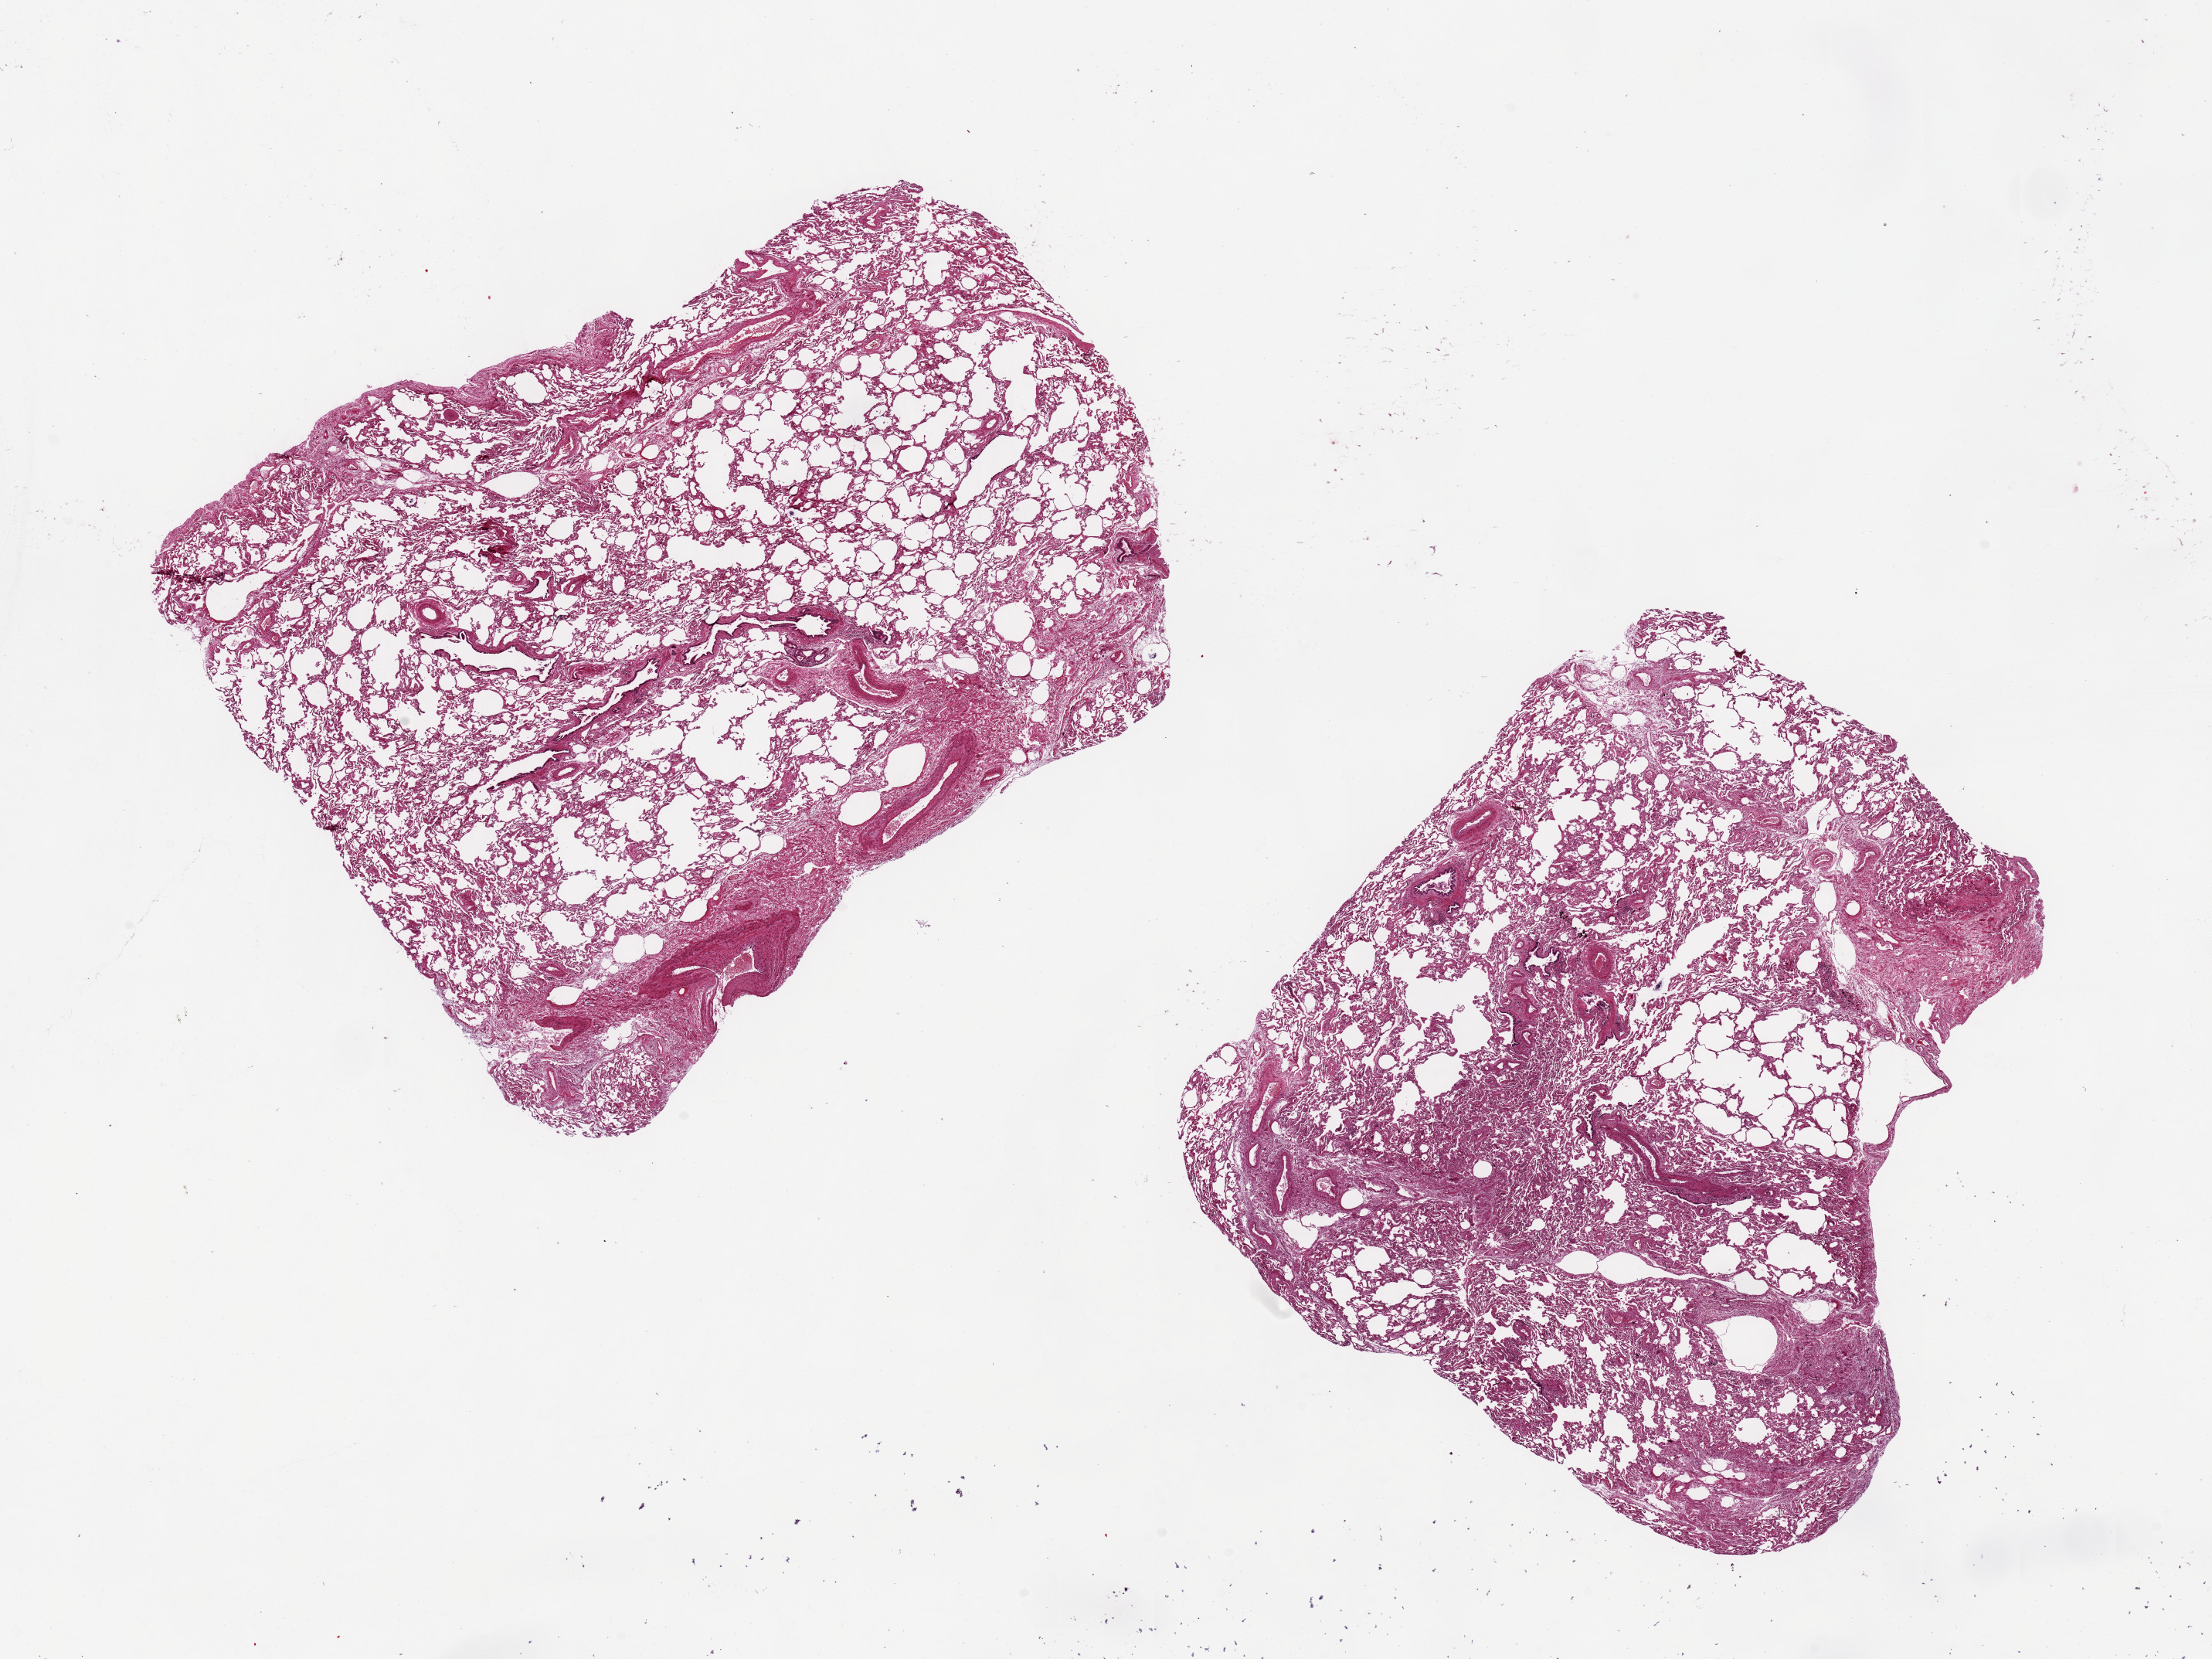
Whole-slide image, H&E stain, shown as a low-resolution overview of the whole scanned area (about 22.6 x 17.0 mm), PAXgene-fixed, paraffin-embedded tissue, sampled site (target tissue): lung, donor tissue sample. Donor: male.
Review note (as recorded): 2 pieces 8x8 mm; no inflammation.